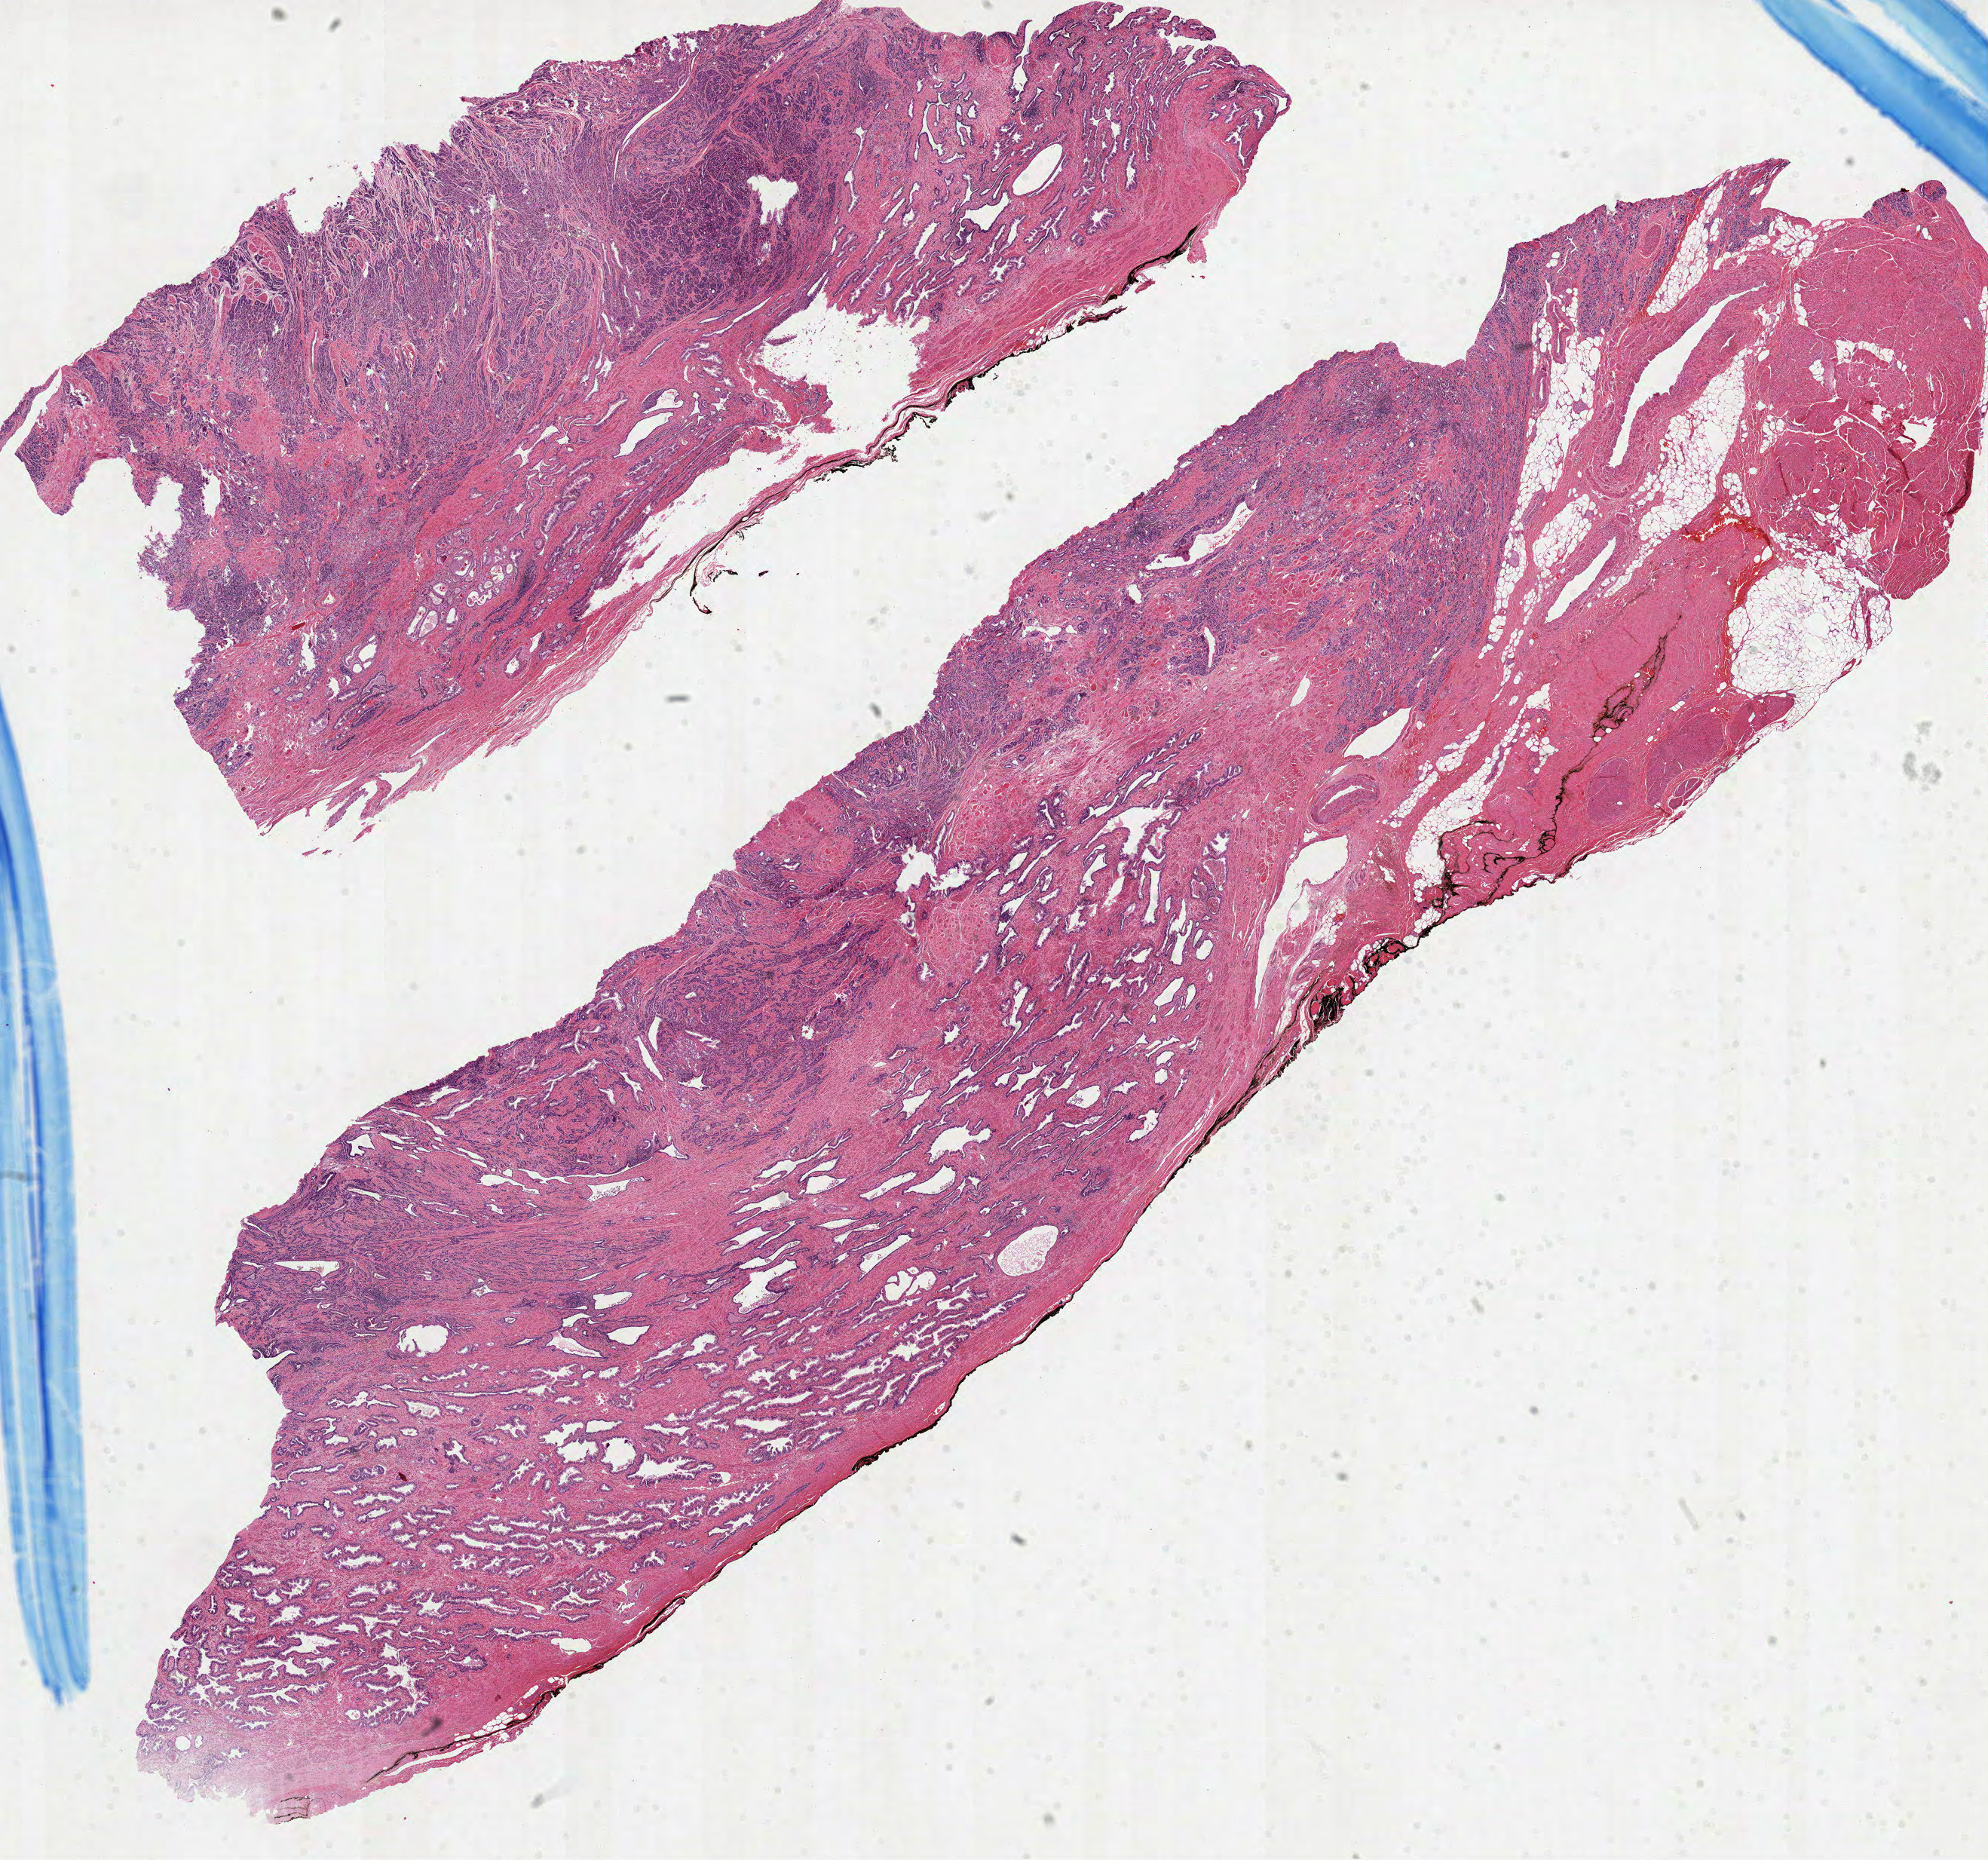
Digitized H&E tissue section (whole slide) — shown as a low-resolution overview of the whole scanned area (about 21.3 x 19.9 mm), formalin-fixed paraffin-embedded (FFPE) diagnostic section, primary tumour sample from the prostate. Male, age 50 years at initial diagnosis. Gleason score: 7 (4+3).
Laterality: bilateral. Lymph nodes positive (case pathology): 0 of 17 examined. Diagnosis: Acinar cell carcinoma (prostate gland).